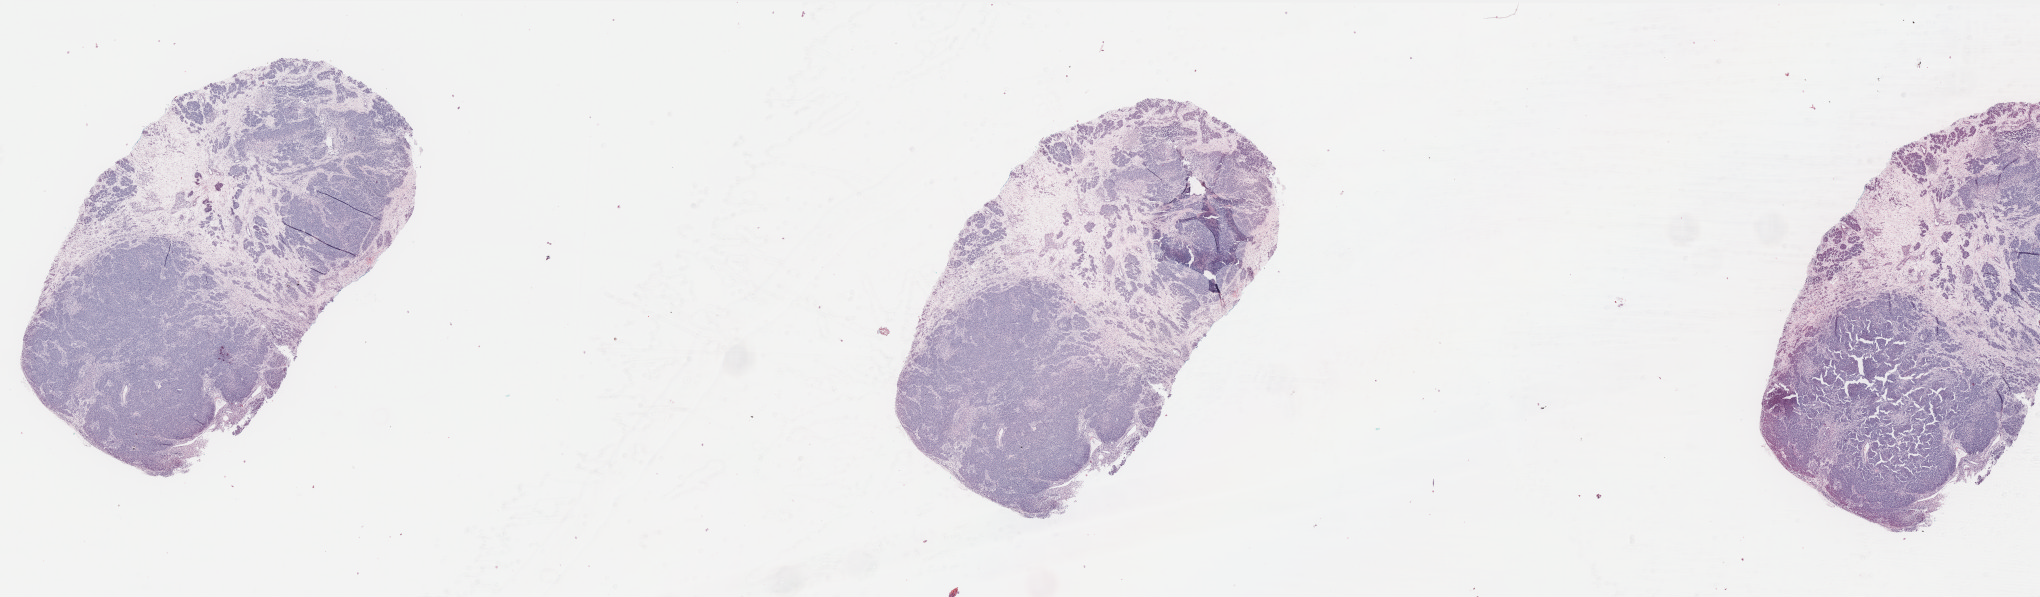
Whole-slide histology image, H&E-stained, whole scanned area (about 32.7 x 9.6 mm) shown as a low-resolution overview; formalin-fixed paraffin-embedded (FFPE) diagnostic section; skin, primary tumour sample. Male, age 45 years at initial diagnosis.
Diagnosis: Malignant melanoma, NOS.